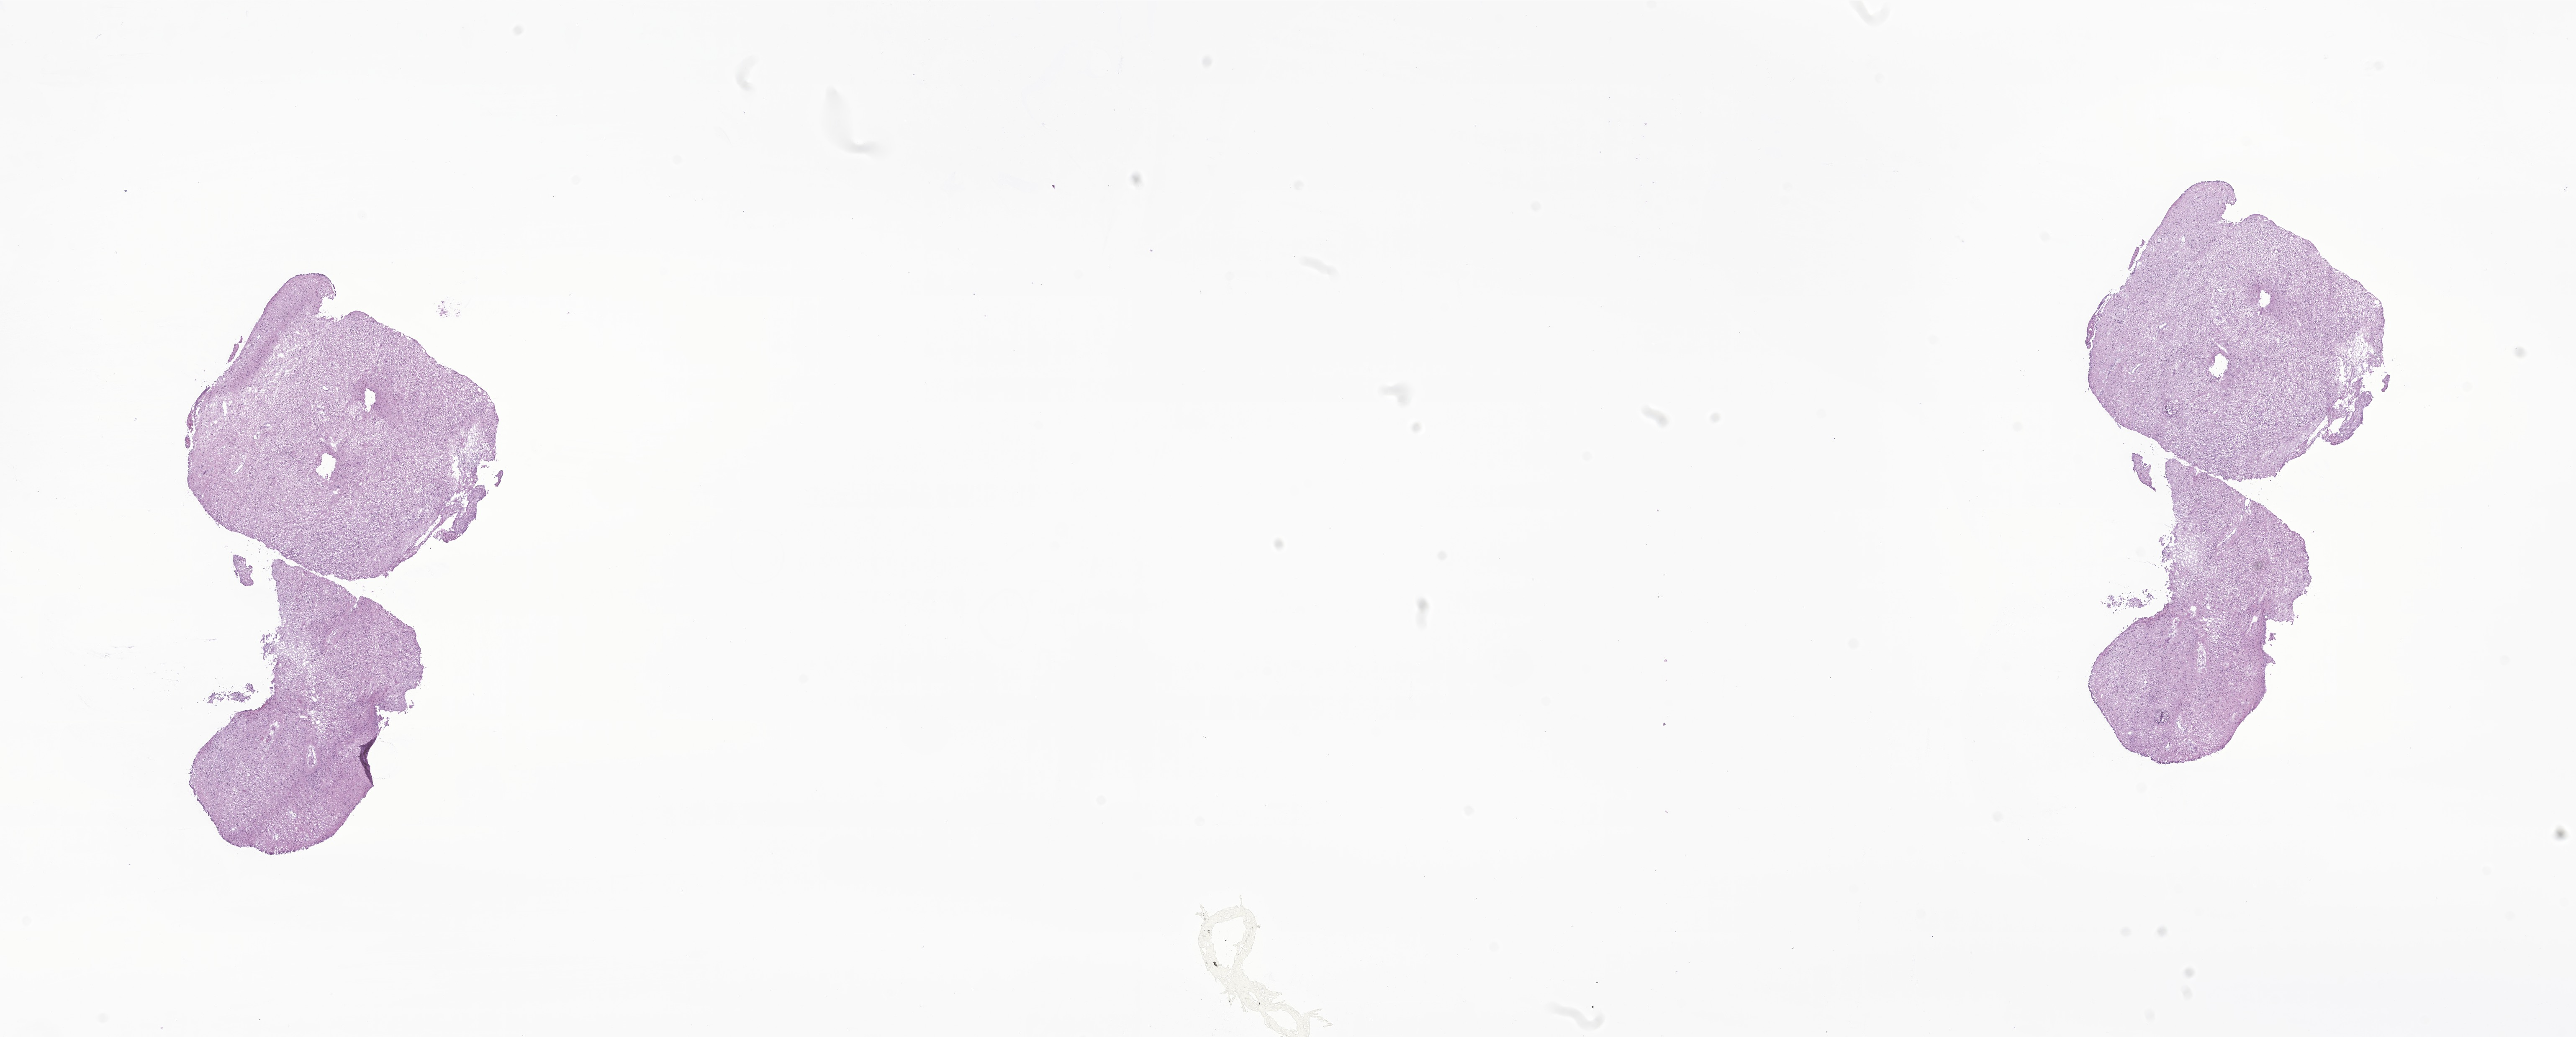
Digitized haematoxylin and eosin-stained section of tumor tissue from the cerebral ventricle — a low-resolution overview of the entire scanned area, about 25.9 x 10.4 mm; frozen section (OCT-embedded). Patient male; age 734 days (about 2.0 years).
- diagnosis (ICD-O-3 morphology term): Ependymoma, NOS